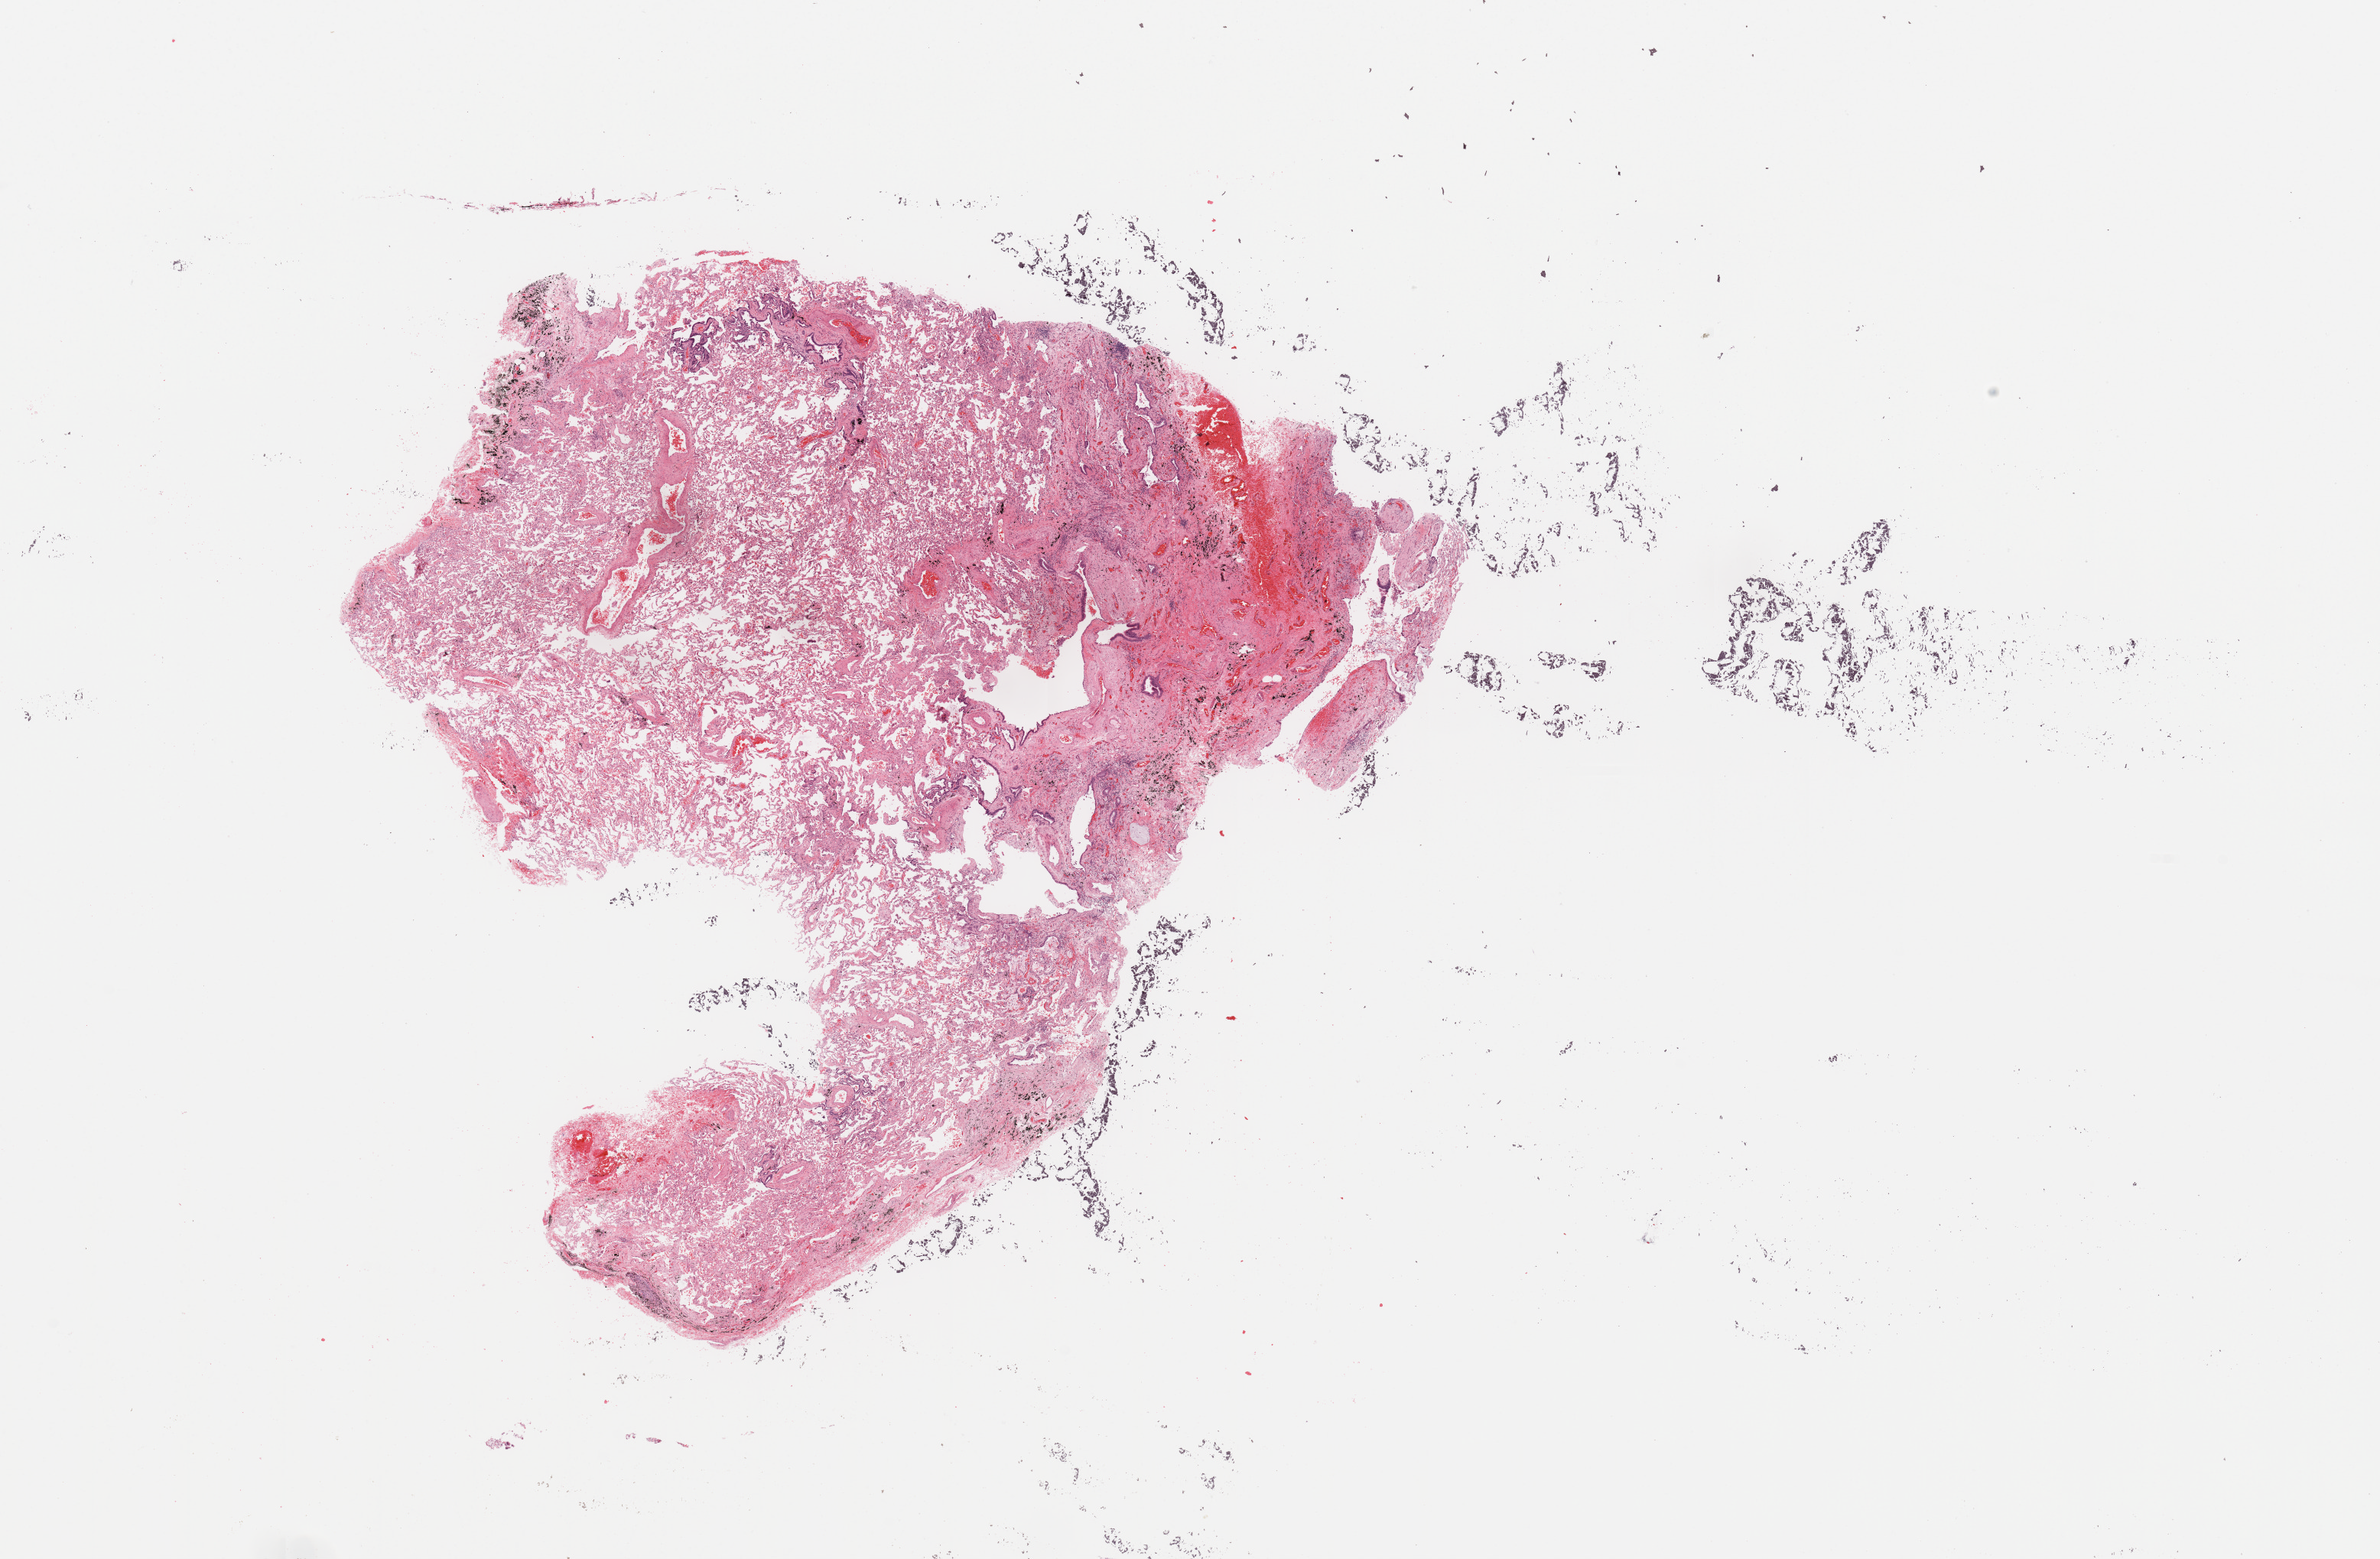
Whole-slide histology image, Hematoxylin and eosin (H&E) stained, low-resolution overview of the scanned area, about 24.6 x 16.1 mm (from a 20x scan); normal (non-tumour) tissue sample, sampled site: lung. Patient: female, age 76 years.
This section: normal (non-tumour) tissue from the same patient. Patient diagnosis: Adenocarcinoma, NOS.